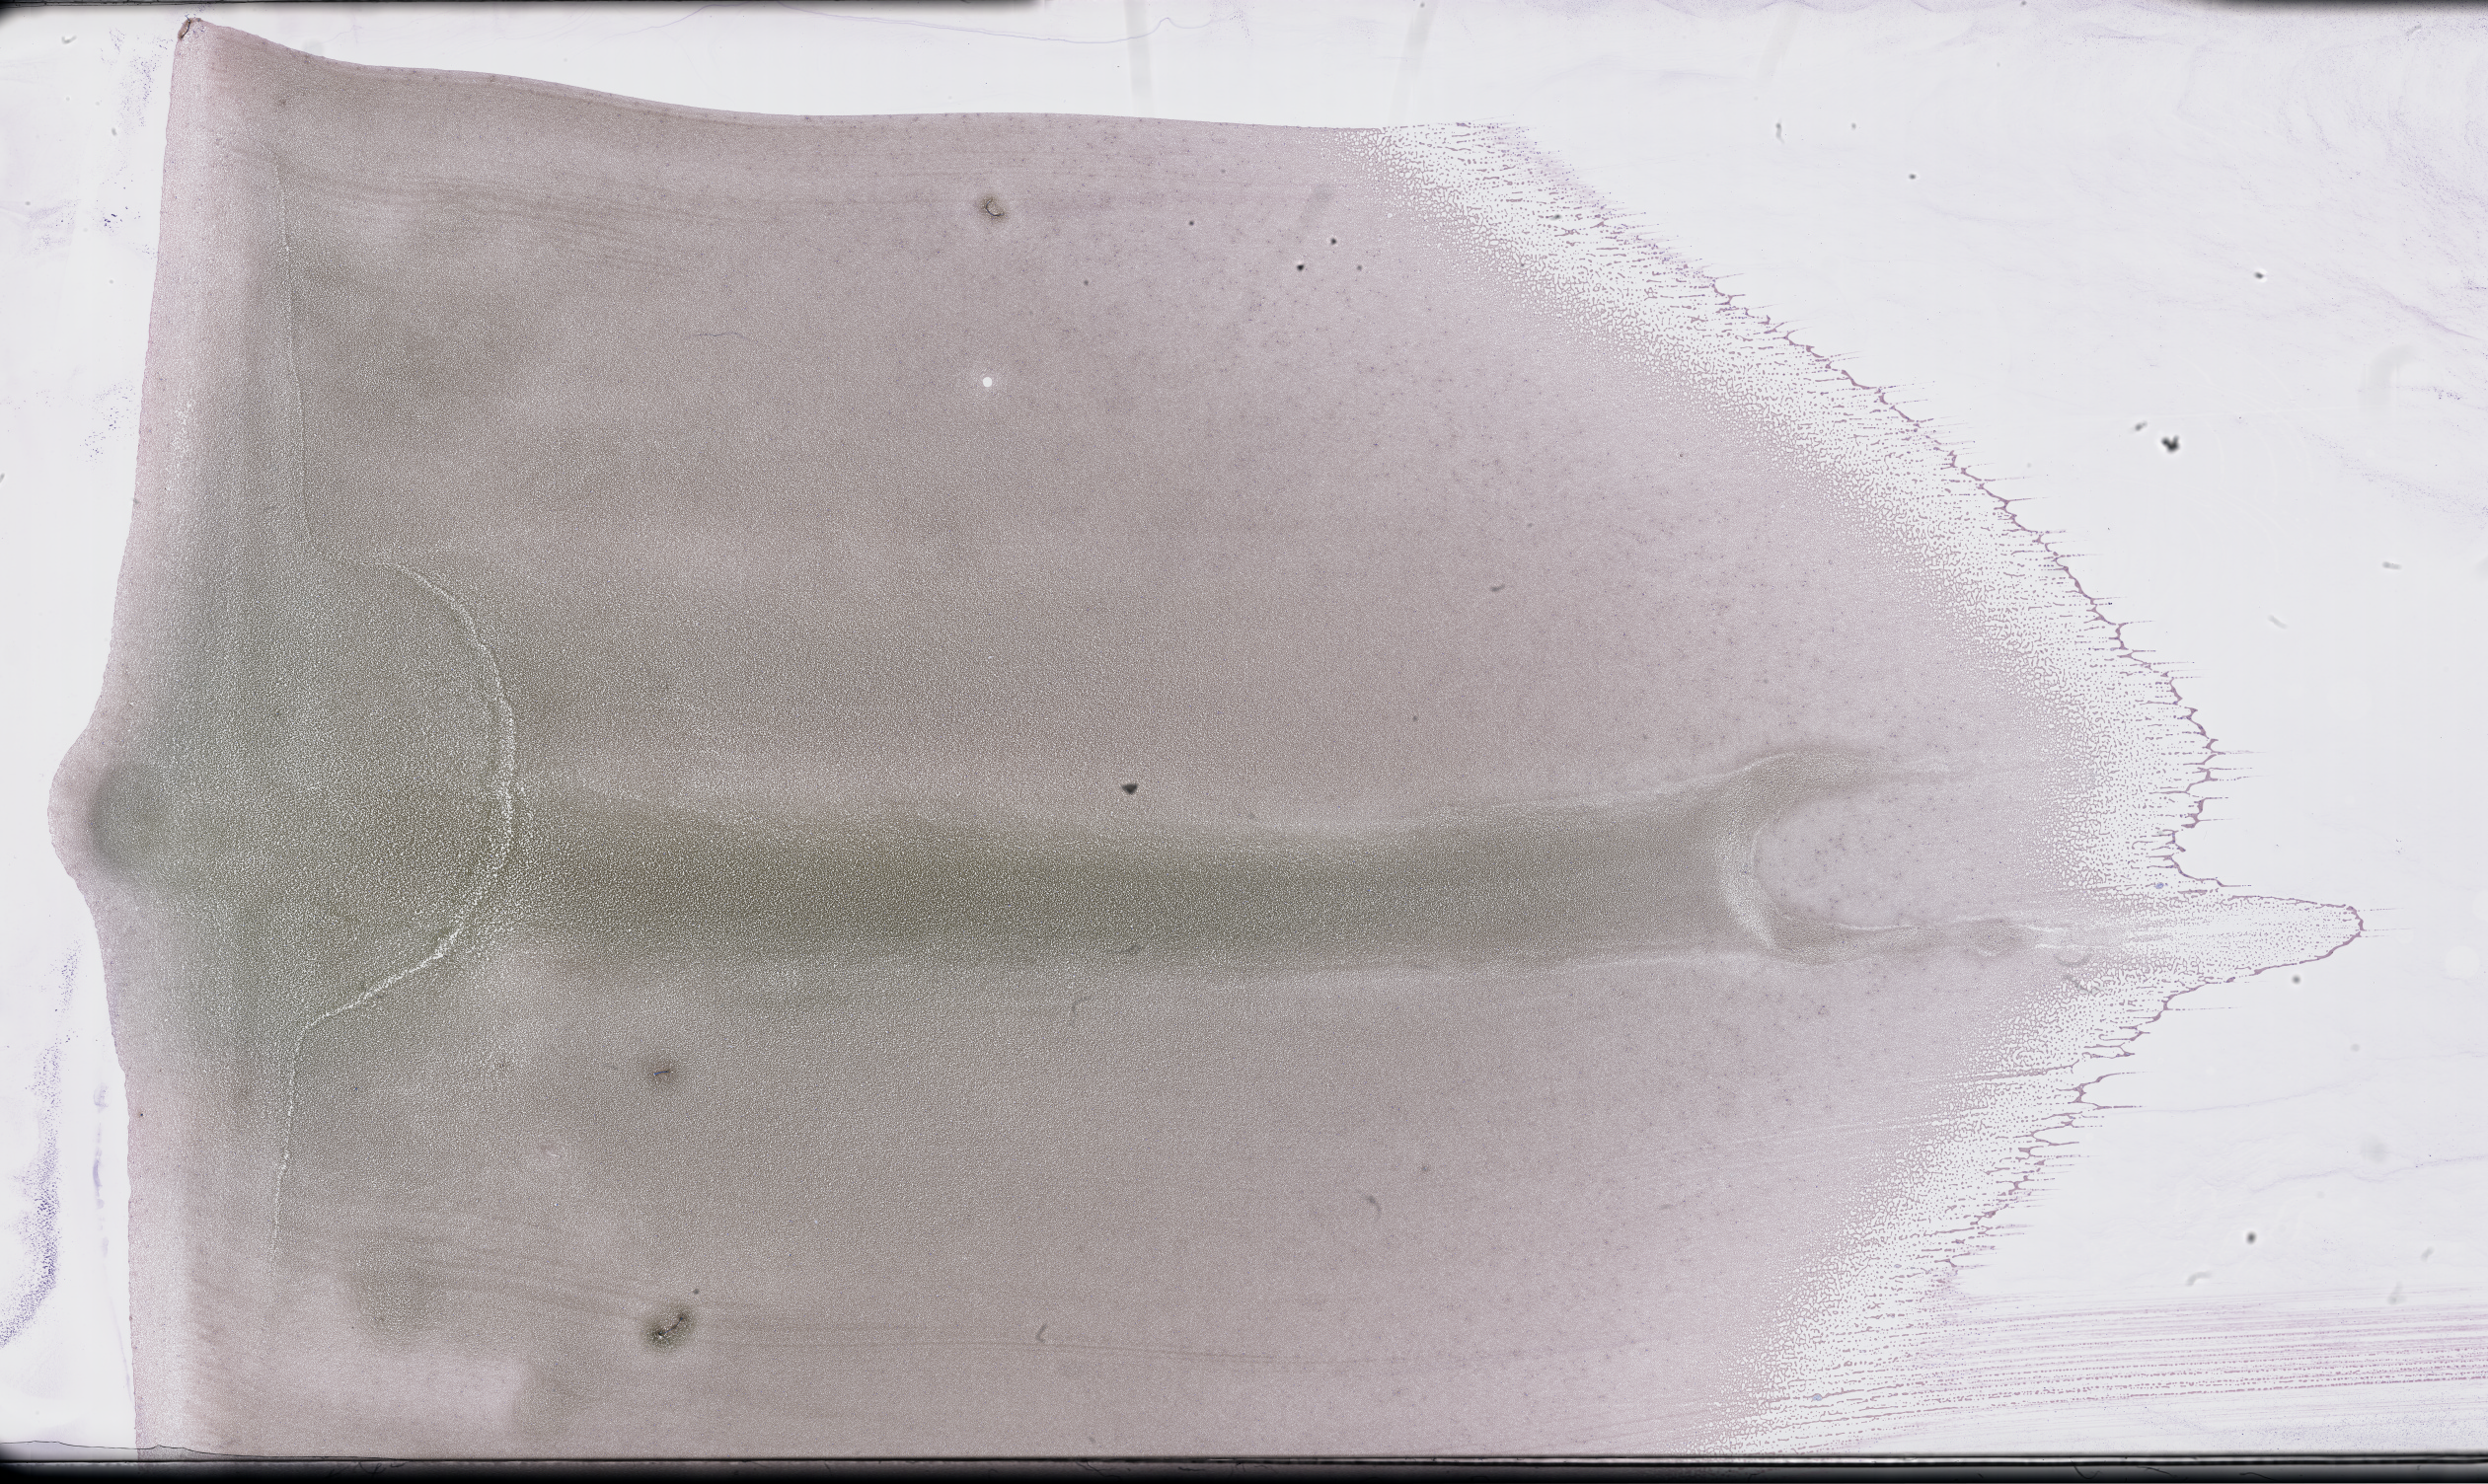
Whole-slide image of a whole blood smear, Wright-Giemsa stain, whole scanned area (about 40.7 x 24.3 mm) shown as a low-resolution overview. Specimen time point: collected on treatment. Patient sex: female.
* from a patient with: Plasma Cell Myeloma